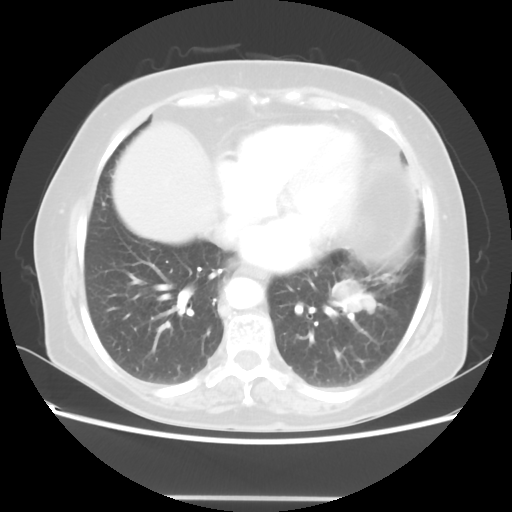
Chest CT, one axial slice. Reconstruction kernel STANDARD. Lung window (W 1500 / L -600 HU). 512 × 512 image matrix, field of view 360 × 360 mm. Female patient, age 73 years. From the clinical record (not read from this slice): clinical TNM (as recorded): T1c N0 M0.
Annotated regions visible in this slice (bounding box drawn by a radiologist):
- lung tumour (recorded histology: adenocarcinoma): box from (x=331, y=275) to (x=380, y=318) px